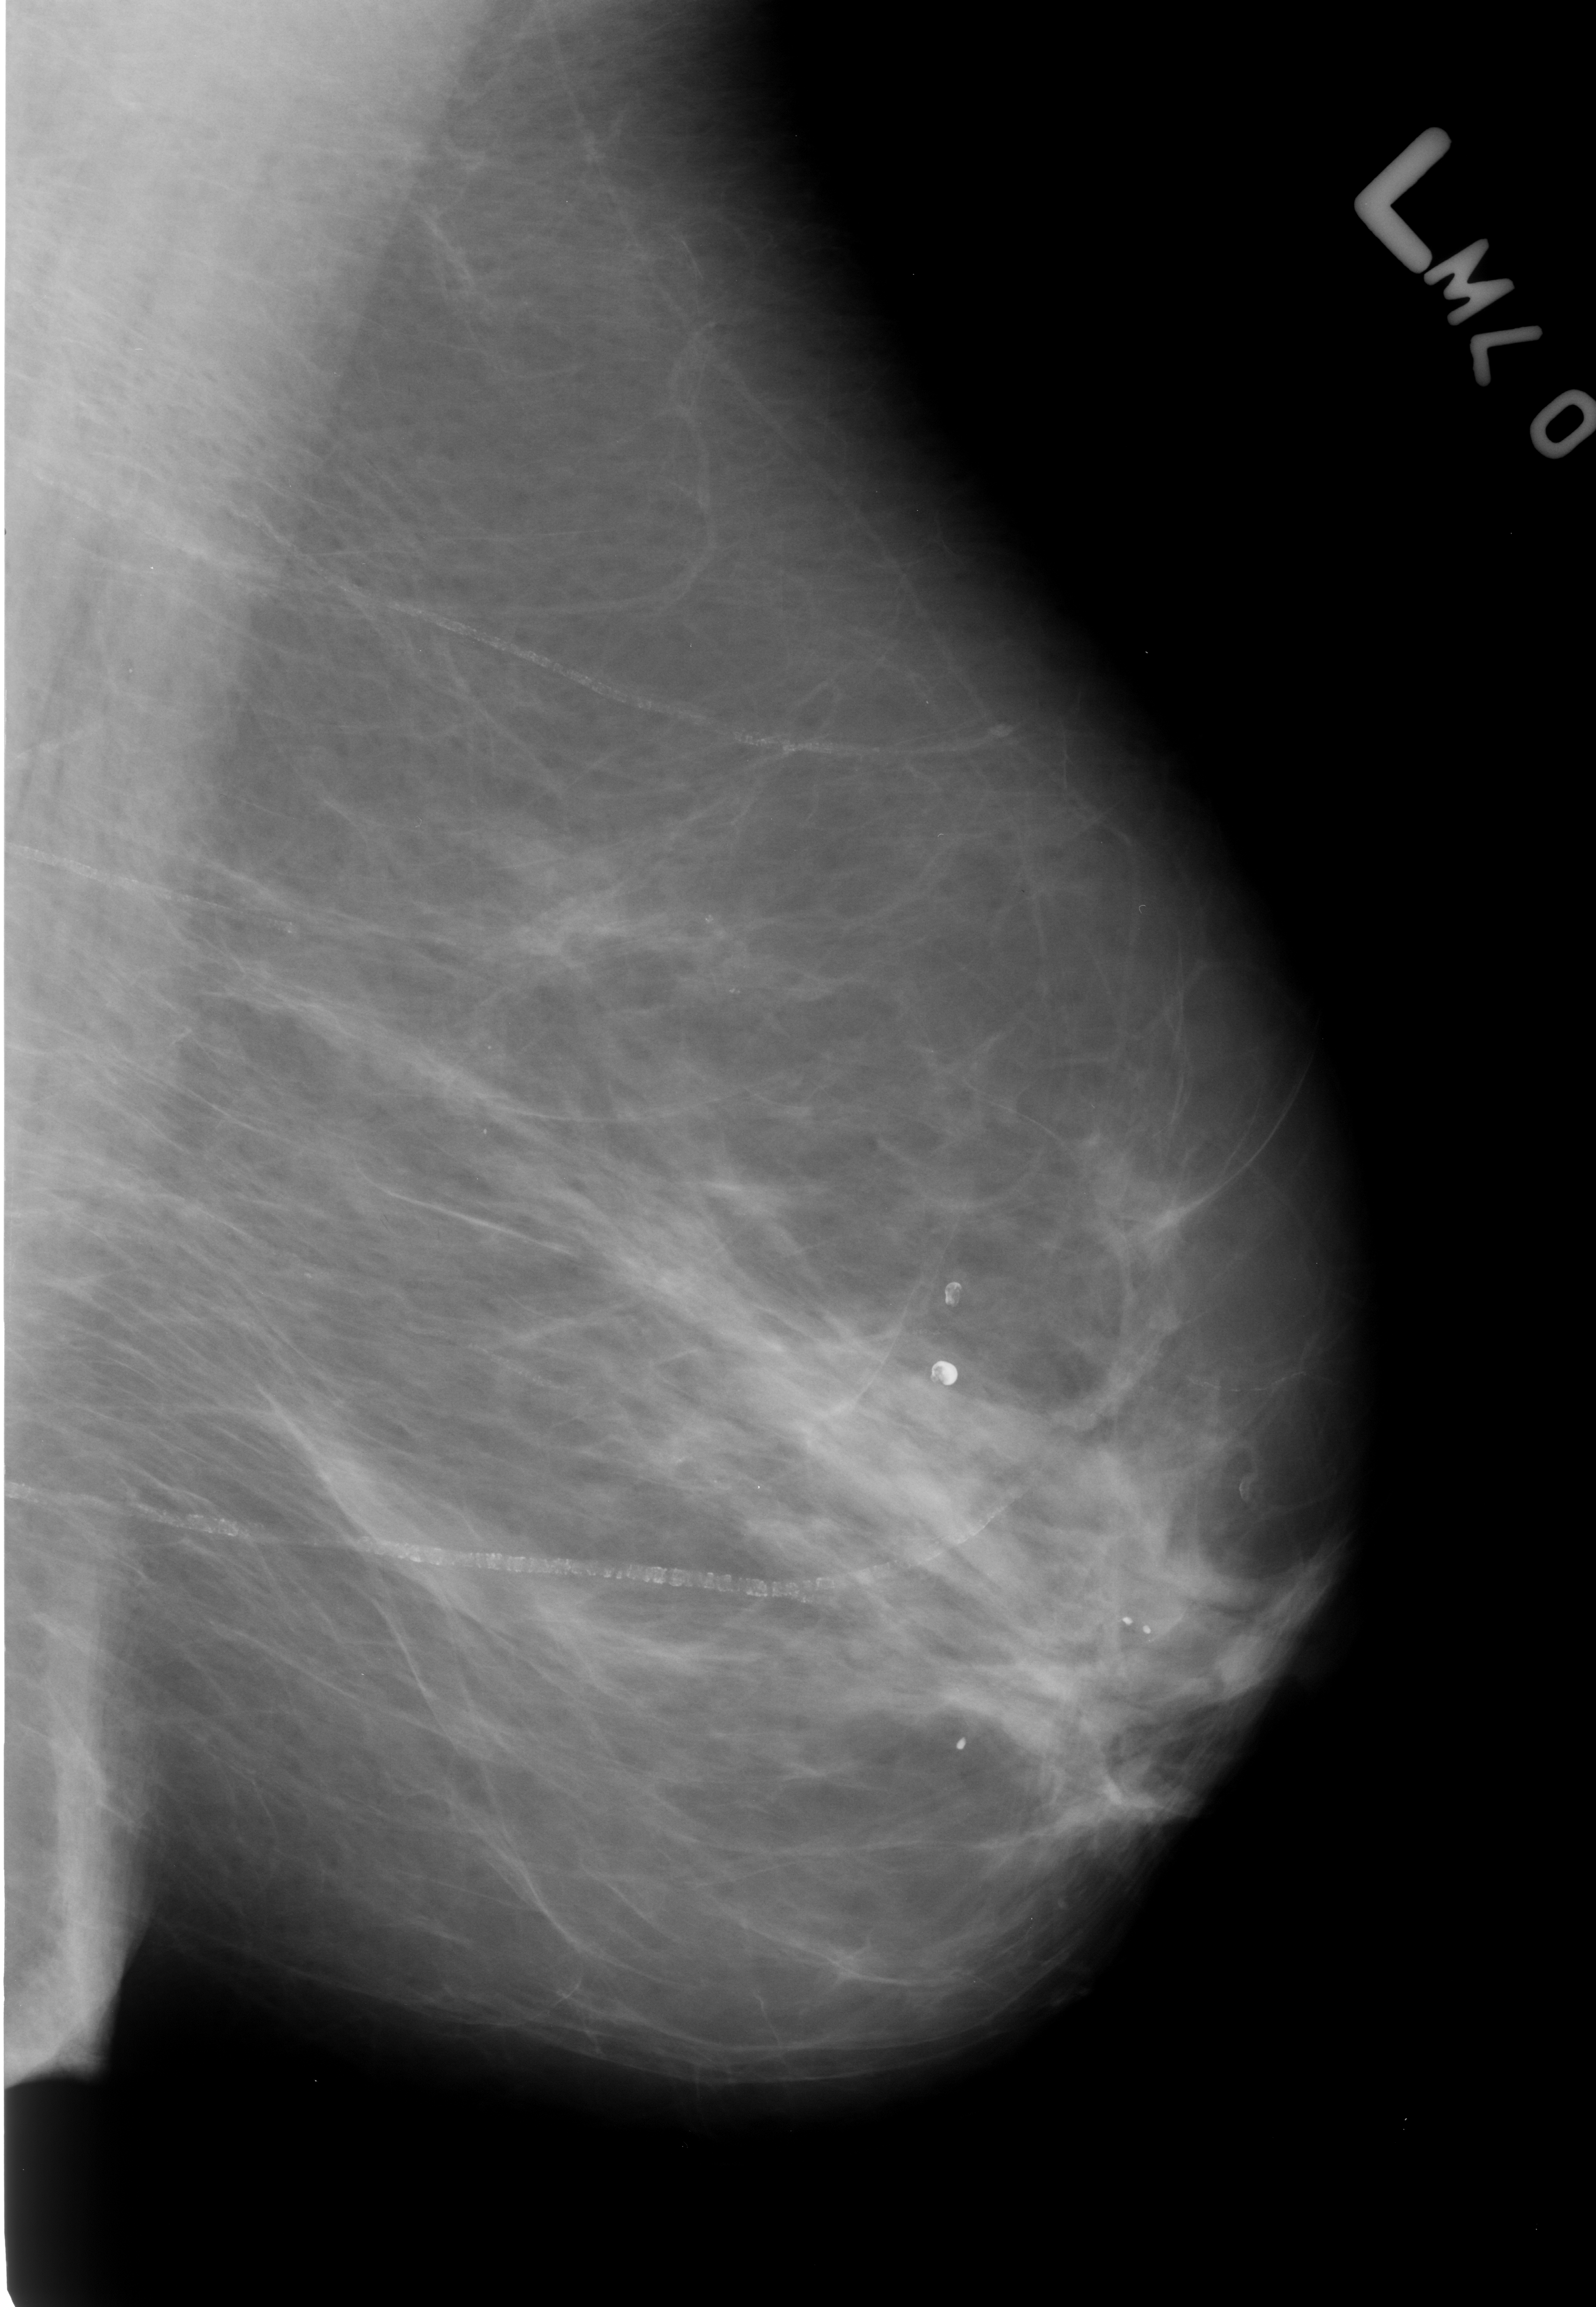
Digitized screen-film mammogram; left breast; mediolateral oblique (MLO) view; BI-RADS breast density category 2 (scale 1–4); 1596 × 2307 image matrix.
Marked abnormalities (boxes around the expert regions of interest):
- Finding 1 of 4: calcifications, morphology vascular / coarse / lucent centered; BI-RADS assessment category 2; outcome (as recorded, no biopsy): benign without callback (not worked up further): bounding box [x1, y1, x2, y2] px = [0, 407, 1028, 787]
- Finding 2 of 4: calcifications, morphology vascular / coarse / lucent centered; BI-RADS assessment category 2; outcome (as recorded, no biopsy): benign without callback (not worked up further): [0, 1359, 1127, 1622]
- Finding 3 of 4: calcifications, morphology vascular / coarse / lucent centered; BI-RADS assessment category 2; outcome (as recorded, no biopsy): benign without callback (not worked up further): [922, 1267, 986, 1323]
- Finding 4 of 4: calcifications, morphology vascular / coarse / lucent centered; BI-RADS assessment category 2; subtlety rating 5 on a 1 (subtle) to 5 (obvious) scale; benign; no additional work-up was recommended (outcome (as recorded, no biopsy): benign without callback): [922, 1350, 978, 1410]